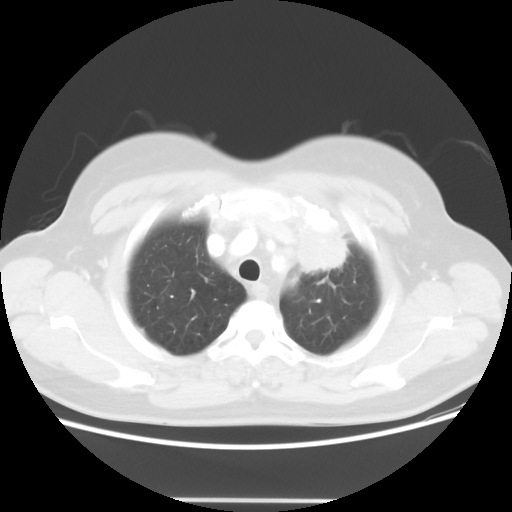
Chest CT, one axial slice; slice 45 of 52 in the series (ordered by position); reconstruction kernel STANDARD; lung window (W 1500 / L -600 HU); 512 × 512 image matrix, field of view 382 × 382 mm. Female patient, age 52 years. Case-level facts recorded for this patient, not image findings: clinical TNM (as recorded): T2 N3 M0.
Outlined on this slice (rectangle marked by the reading radiologist):
- lung tumour (recorded histology: adenocarcinoma): bounding box <290,215,354,277> (left, top, right, bottom; pixels)